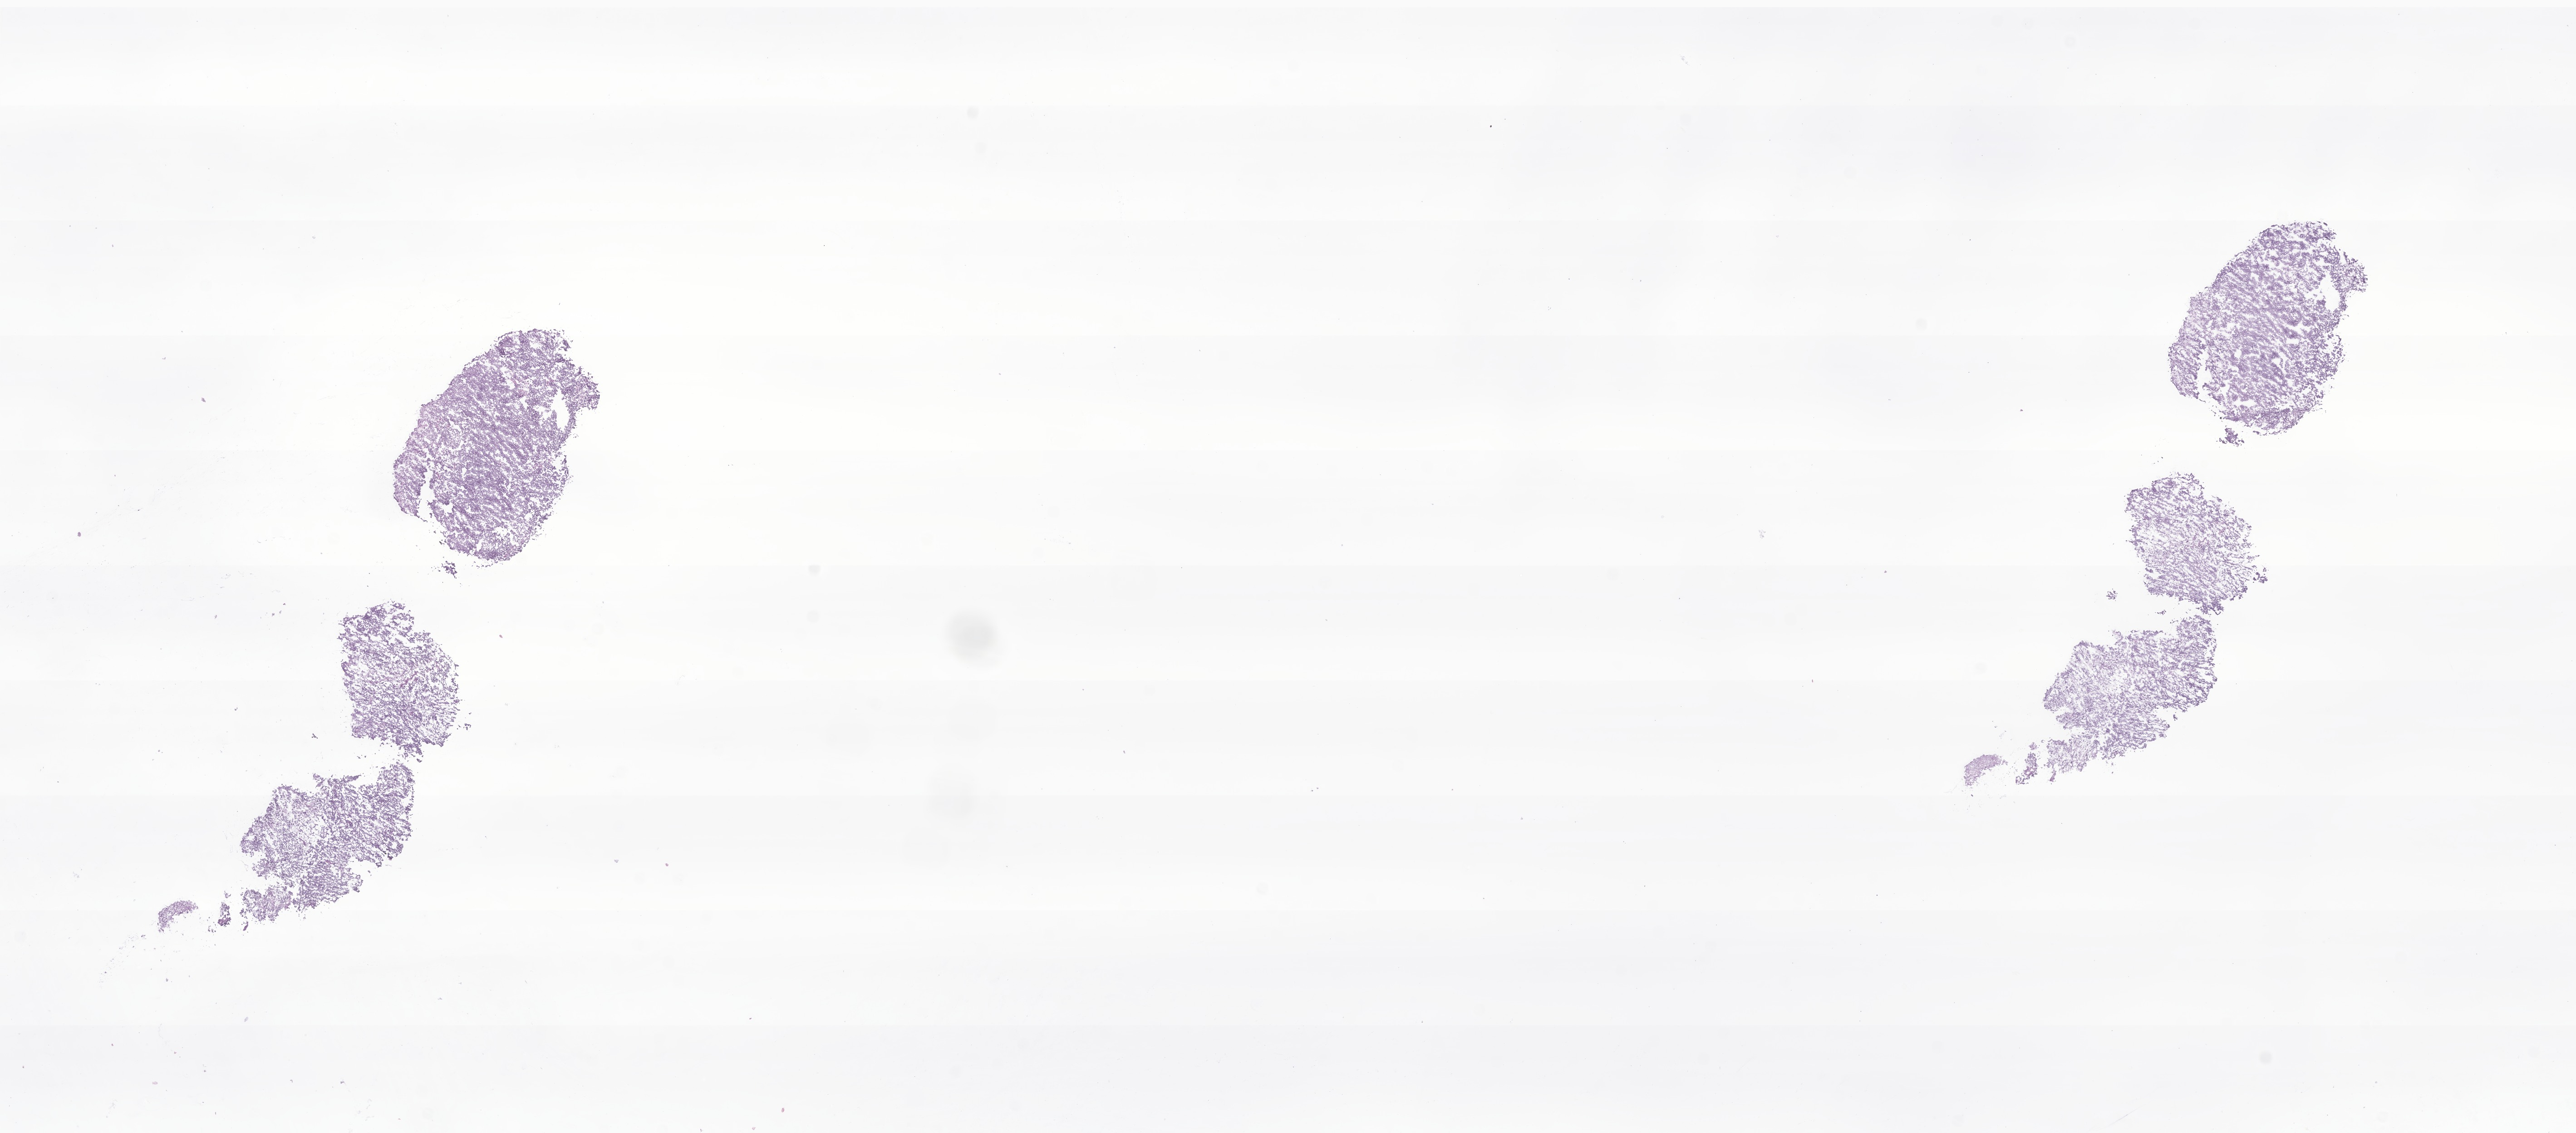
Whole-slide image, hematoxylin and eosin (H&E) stain of tumor tissue from the brain — low-resolution overview of the scanned area, about 23.9 x 10.5 mm; frozen section. Male patient, age 88 months (7 years 4 months).
Diagnosis: Medulloblastoma, NOS.